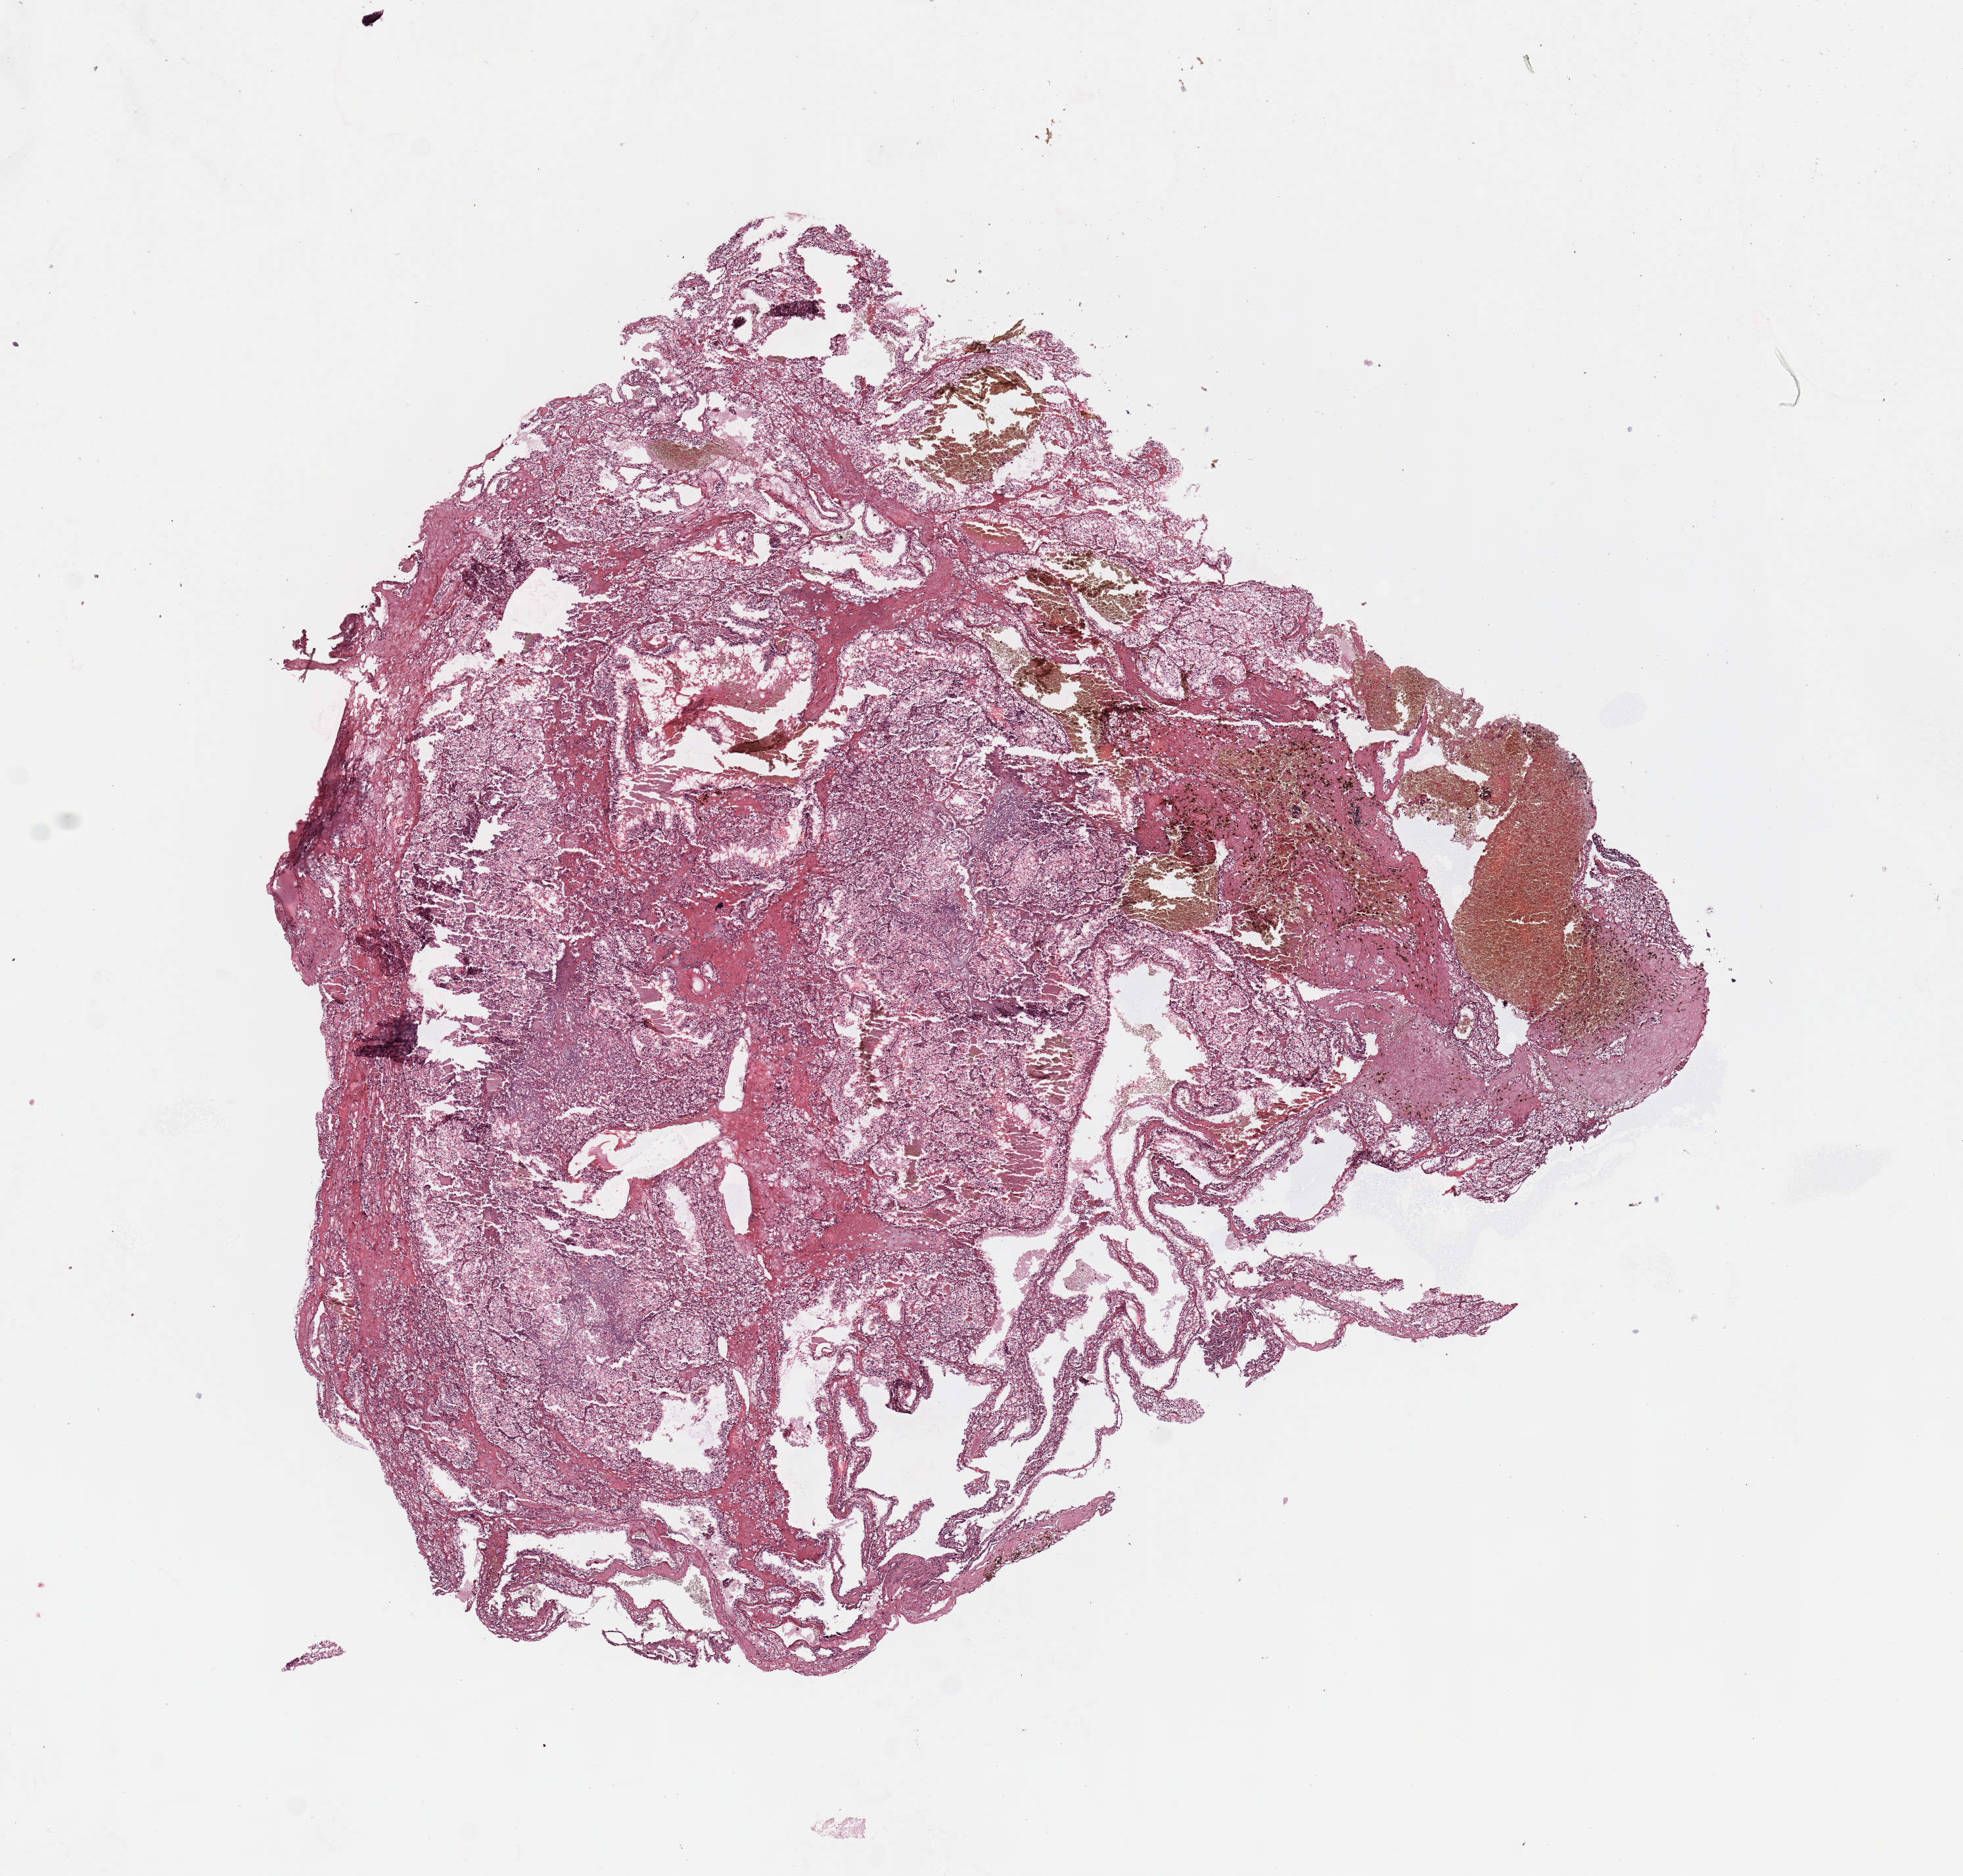
Digitized H&E tissue section (whole slide), whole scanned area (about 11.8 x 11.3 mm, acquisition: 20x scan) shown as a low-resolution overview; tumour tissue sample, sampled site: kidney. Male, 61 y/o.
Diagnosis: Renal cell carcinoma, NOS.